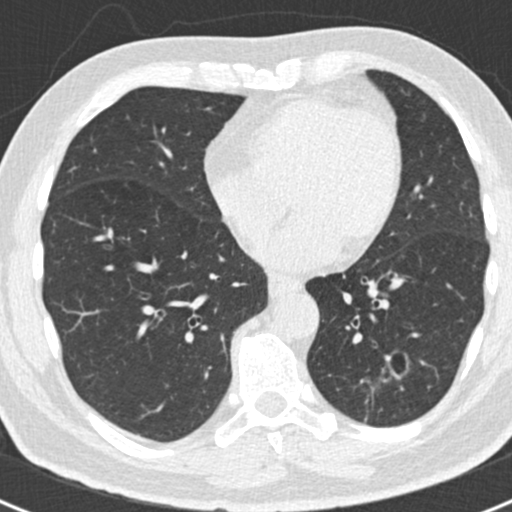
Chest CT (low-dose screening protocol), one axial image; baseline screening round; lung window (W 1500 / L -600 HU); standard (soft-tissue) reconstruction kernel (B30f). Male participant, aged 66 years at enrolment. Former smoker at enrolment.
Expert-annotated lung lesion, box from (x=341, y=336) to (x=419, y=414) px. Reader record for this screening exam (exam-level; its link to the box is not recorded): non-calcified nodule or mass ≥4 mm, left lower lobe, 43 × 27 mm, smooth margins.